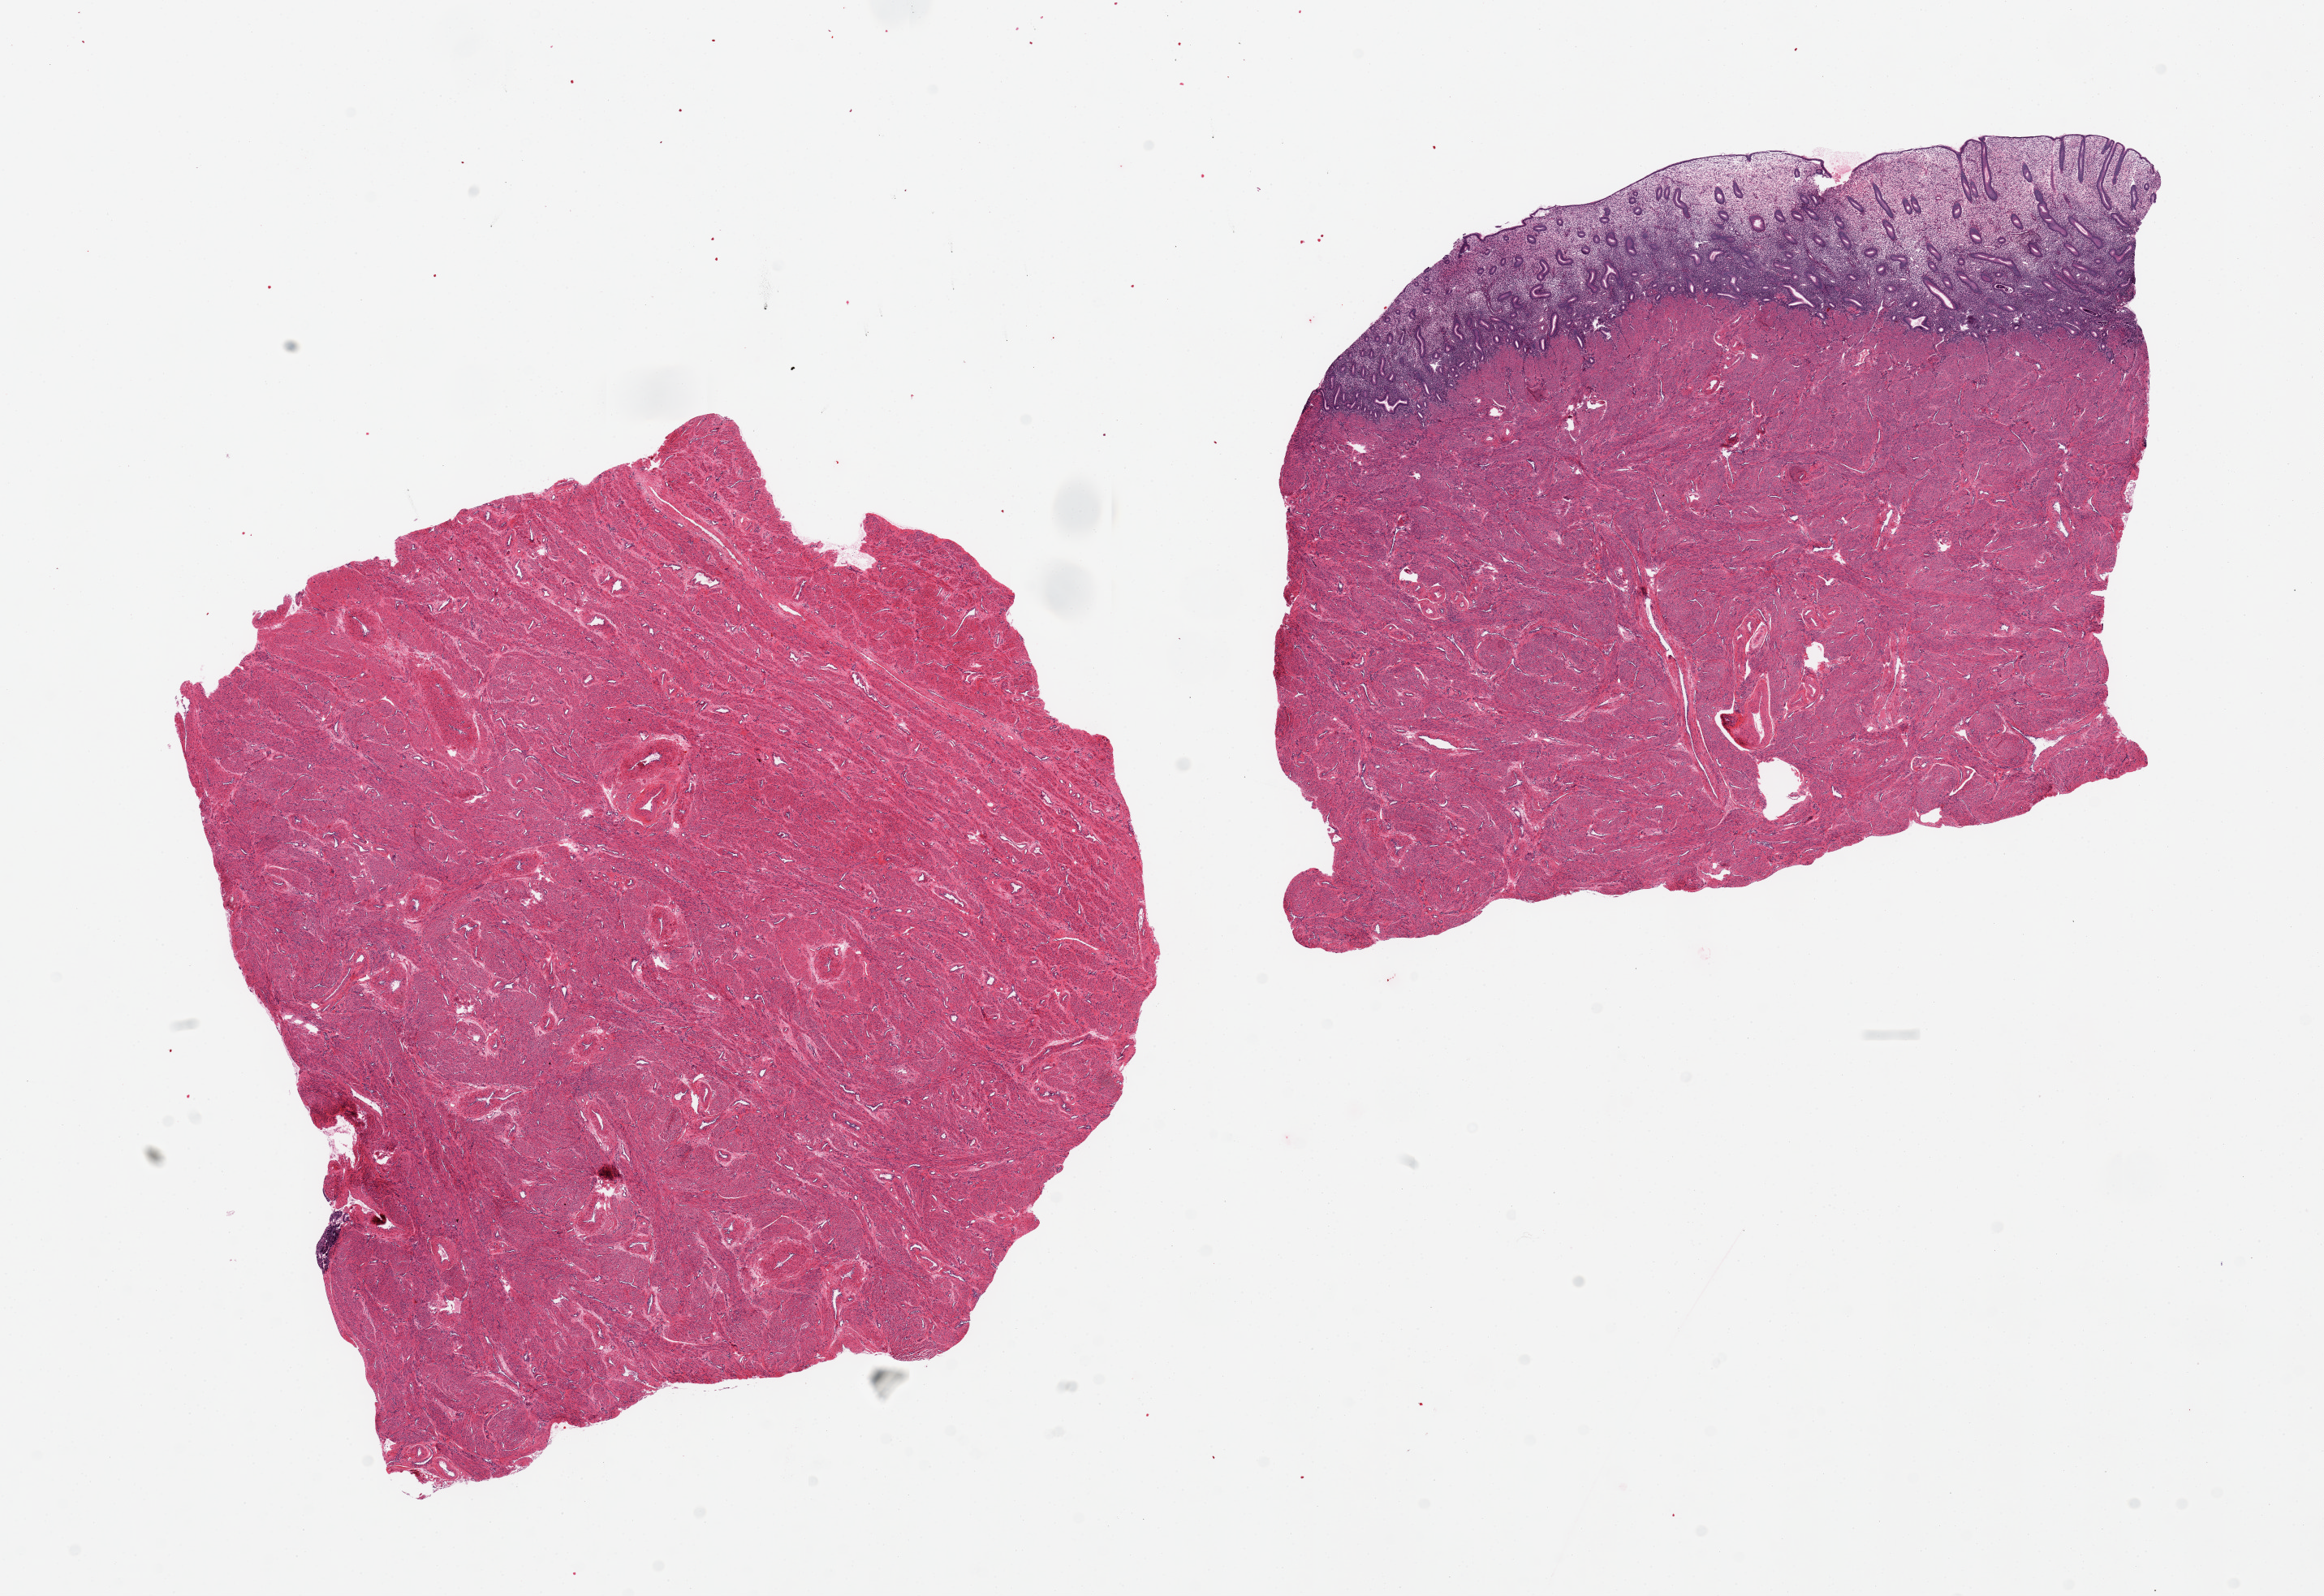
Digitized H&E-stained section, whole scanned area (about 22.6 x 15.5 mm) shown as a low-resolution overview. PAXgene-fixed paraffin-embedded (PFPE) section. Sampled site (target tissue): uterus. Donor tissue sample.
- pathologist's review note for this sample: 2 pieces, one piece is essentially all myometrium, second is 20% endometrium/80% myometrium